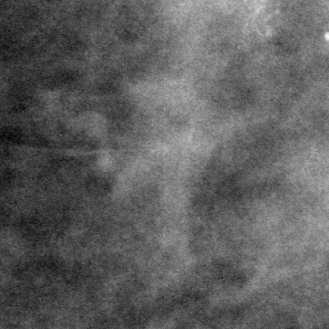
Crop from a digitized film mammogram around one marked abnormality, left breast, CC view.
Finding: calcifications, morphology amorphous, distribution clustered; BI-RADS assessment category 4; pathology result (as recorded, not read from the image): benign.